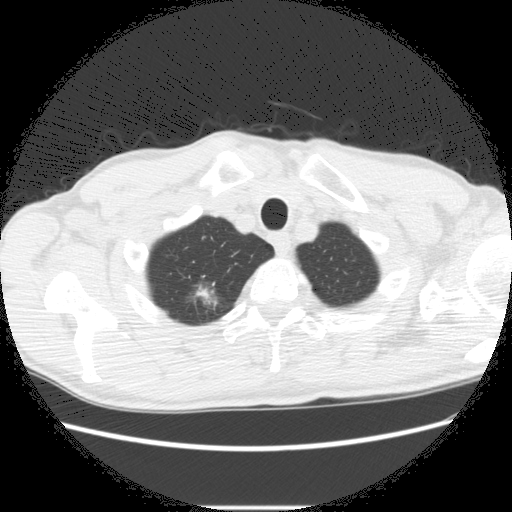
Axial slice from a low-dose chest CT screening exam. Second screening round (one year after baseline). Lung window (W 1500 / L -600 HU). 2.5 mm slice thickness. Standard (soft-tissue) reconstruction kernel (STANDARD). 512 × 512 image matrix. Male participant, aged 66 years at enrolment. Former smoker at enrolment.
Lesion marked by an expert reader, box from (x=171, y=277) to (x=233, y=327) px. The screening reader recorded 5 non-calcified nodules or masses ≥4 mm on this exam (right lower lobe, right upper lobe, right upper lobe, right upper lobe, left lower lobe); which of them this box marks is not recorded. Official screen result: positive, change unspecified: nodule(s) >= 4 mm or enlarging nodule(s), mass(es), or other non-specific abnormalities suspicious for lung cancer. Lung cancer was diagnosed 75 days after this screen: adenocarcinoma, NOS, right upper lobe, undifferentiated (G4), stage IA (AJCC 6th edition), 20 mm at pathology.